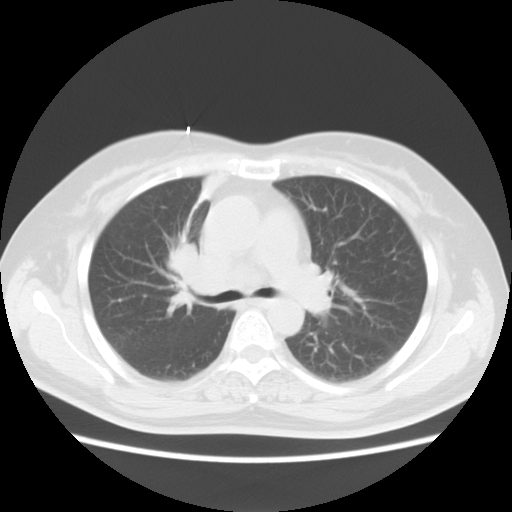
Chest CT, one axial slice; position 6 of 18 along the scan axis; 120 kVp; lung window (W 1500 / L -600 HU); 5 mm slice thickness; 512 × 512 image matrix, field of view 350 × 350 mm. Patient: female, 54 years. Case-level facts recorded for this patient, not image findings: clinical TNM (as recorded): T2 N3 M0; histopathological grade: G3.
Outlined on this slice (rectangle marked by the reading radiologist):
- lung tumour (recorded histology: small cell carcinoma): box from (x=156, y=233) to (x=201, y=302) px